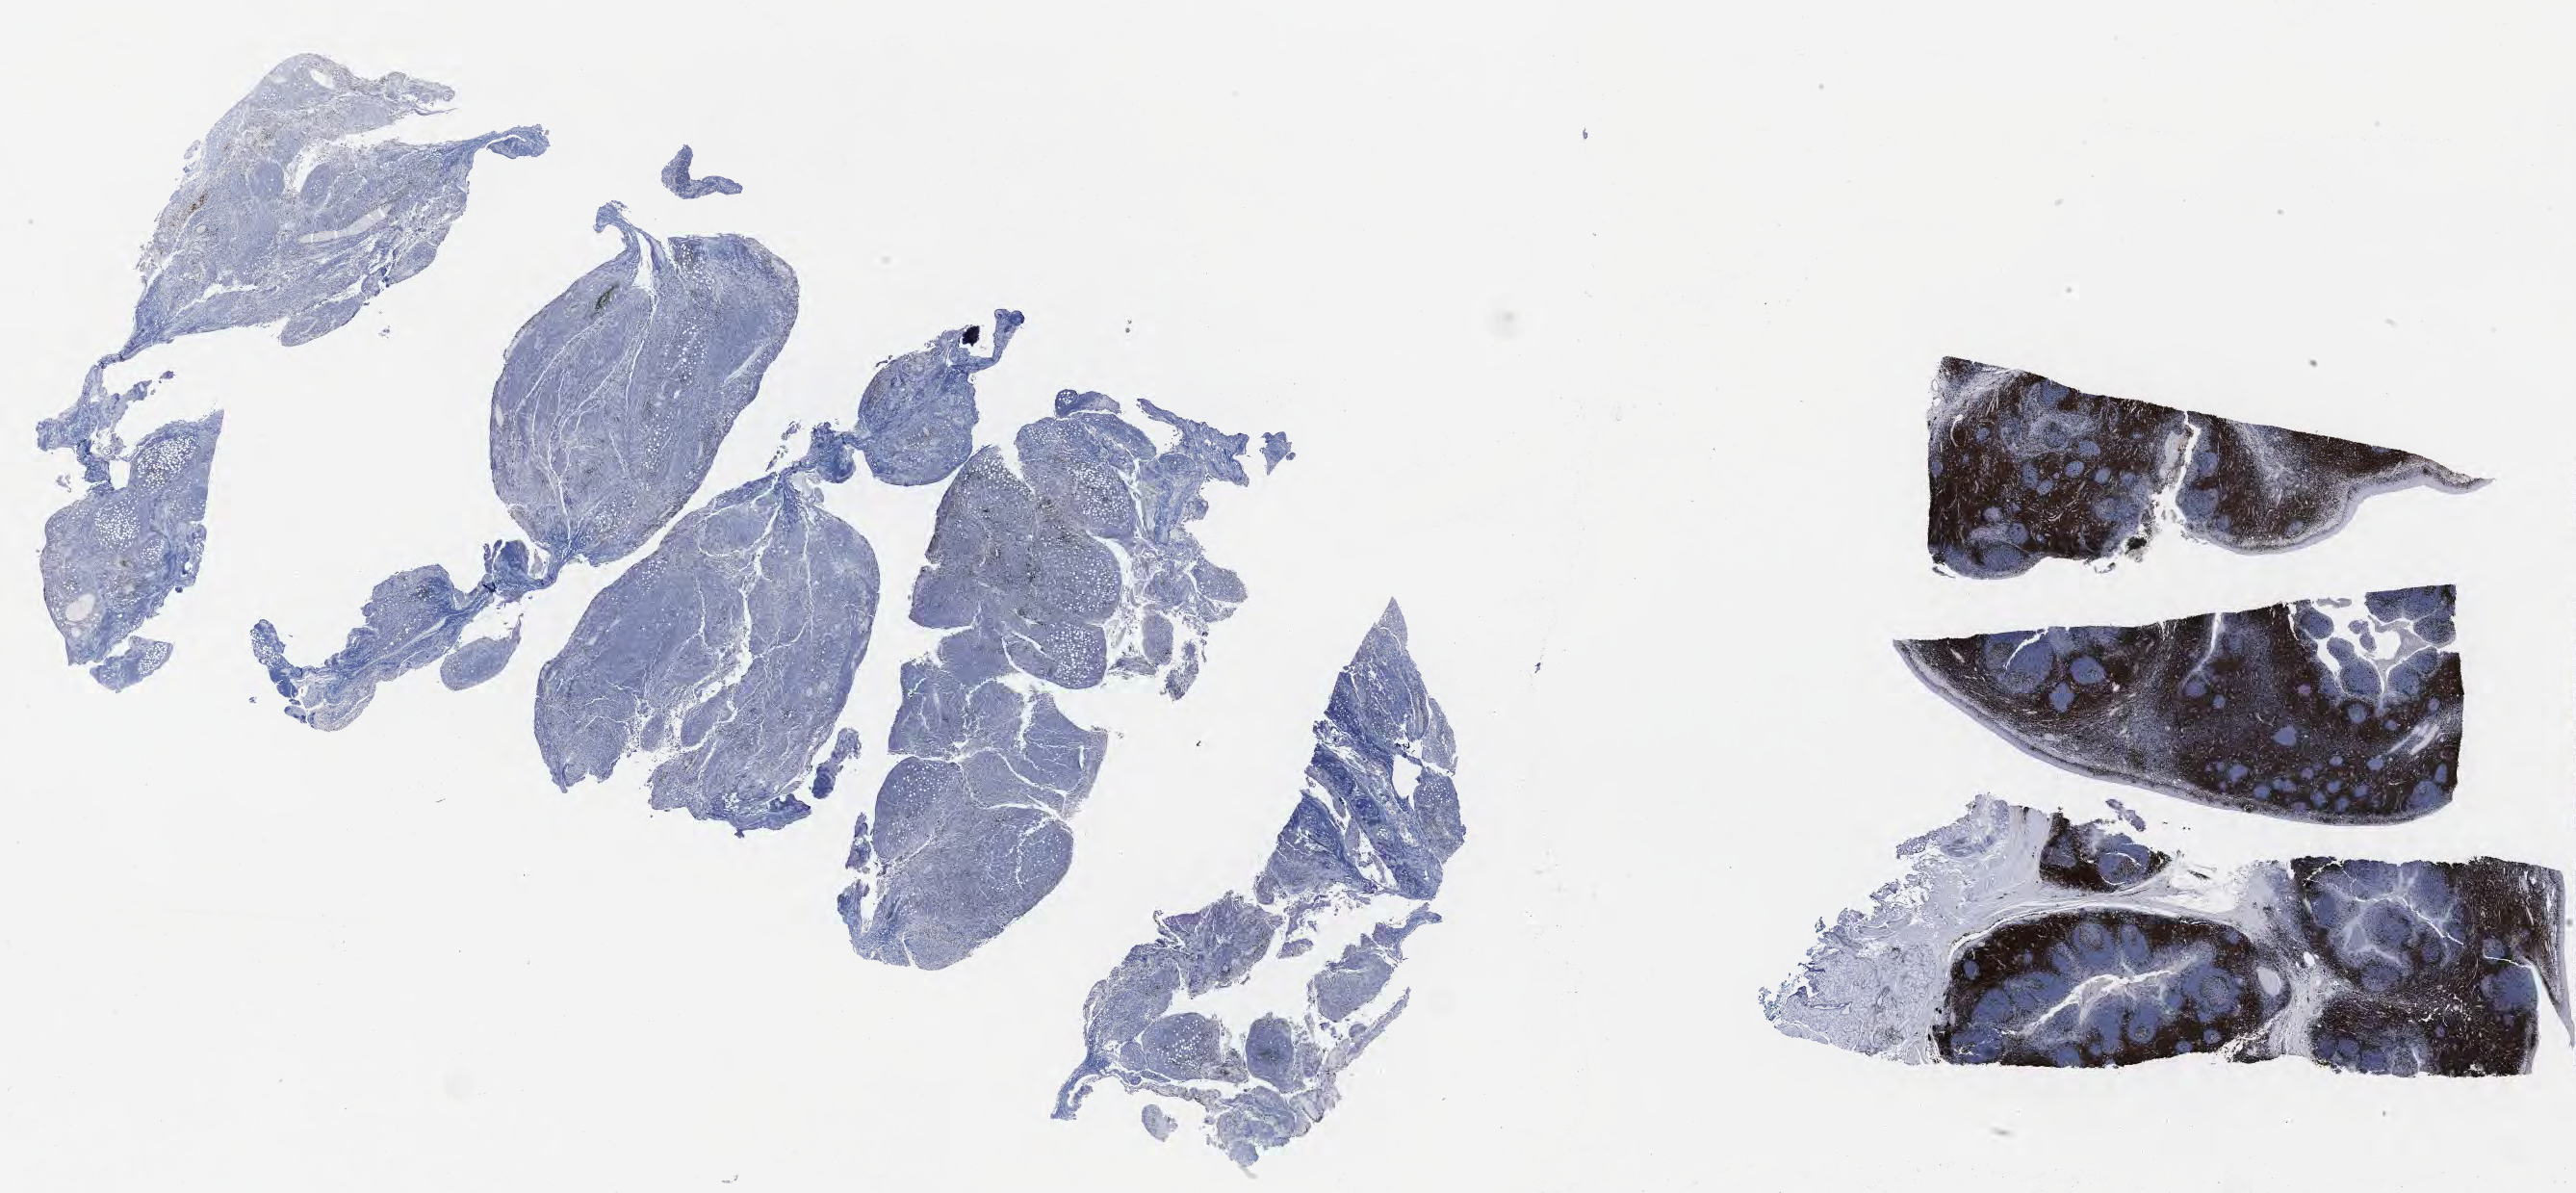
IHC for CD3, whole-slide image, low-resolution overview of the scanned area, about 43.3 x 20.0 mm, specimen: tumor tissue, anatomic site: peritoneum. Patient: male, age at initial diagnosis 8 years.
Diagnosis: Burkitt lymphoma, NOS.